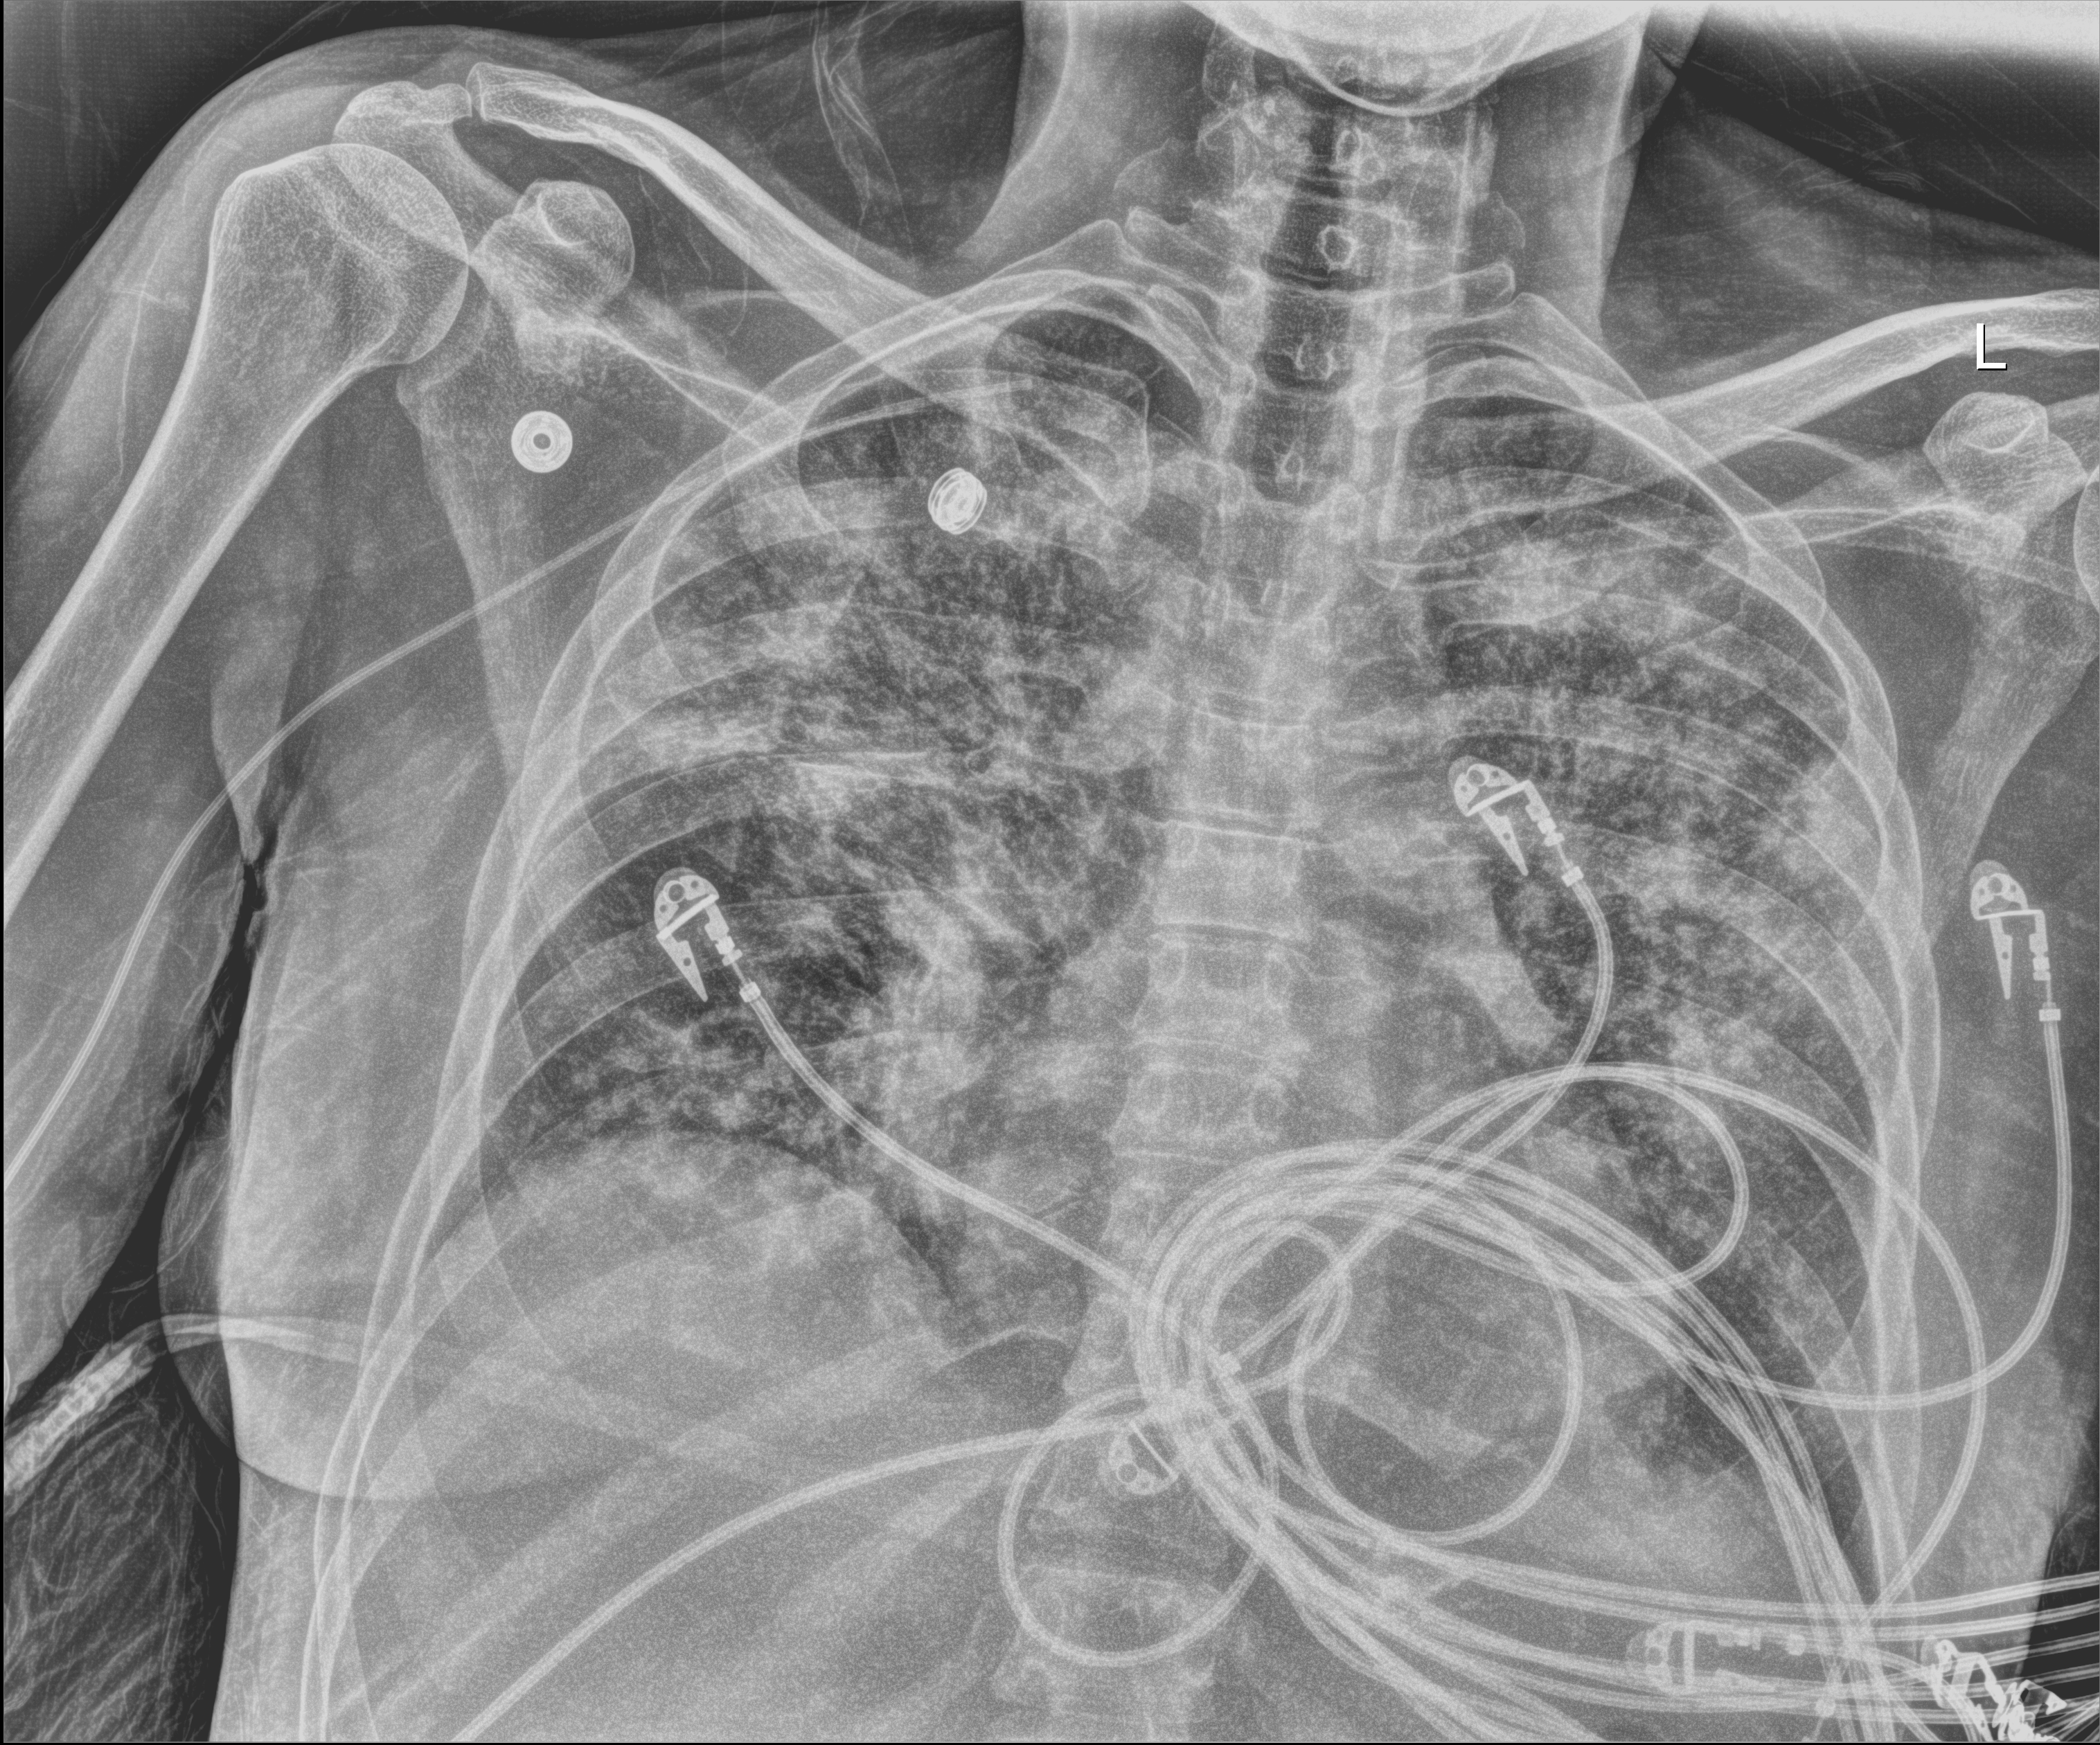
Portable chest radiograph, anteroposterior (AP) projection. Female patient hospitalised with COVID-19, age 18–59 years.
From the hospital-stay record, not from the radiograph (when in the stay this image was taken is not recorded):
- admitted to intensive care during this hospital stay: yes